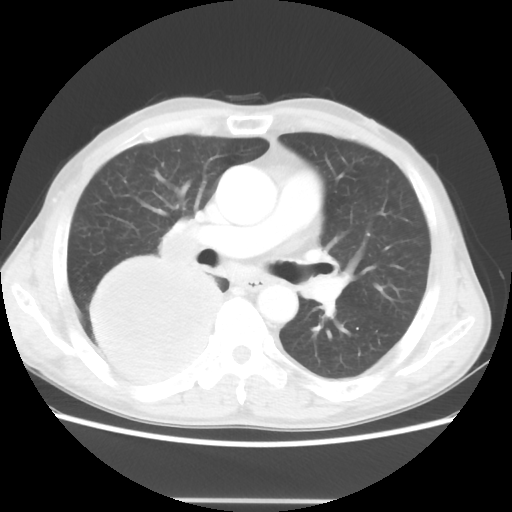
Chest CT, one axial slice. Slice 27 of 48 in the series (ordered by position). Reconstruction kernel STANDARD. 100 kVp. Lung window (W 1500 / L -600 HU). 5 mm slice thickness. 512 × 512 image matrix, field of view 361 × 361 mm. Patient: male, 66 years. From the clinical record (not read from this slice): clinical TNM (as recorded): T4 N1 M1; histopathological grade: G3.
Outlined on this slice (bounding box drawn by a radiologist):
- lung tumour (recorded histology: small cell carcinoma): bounding box (x1, y1, x2, y2) in pixels: (82, 248, 220, 392)